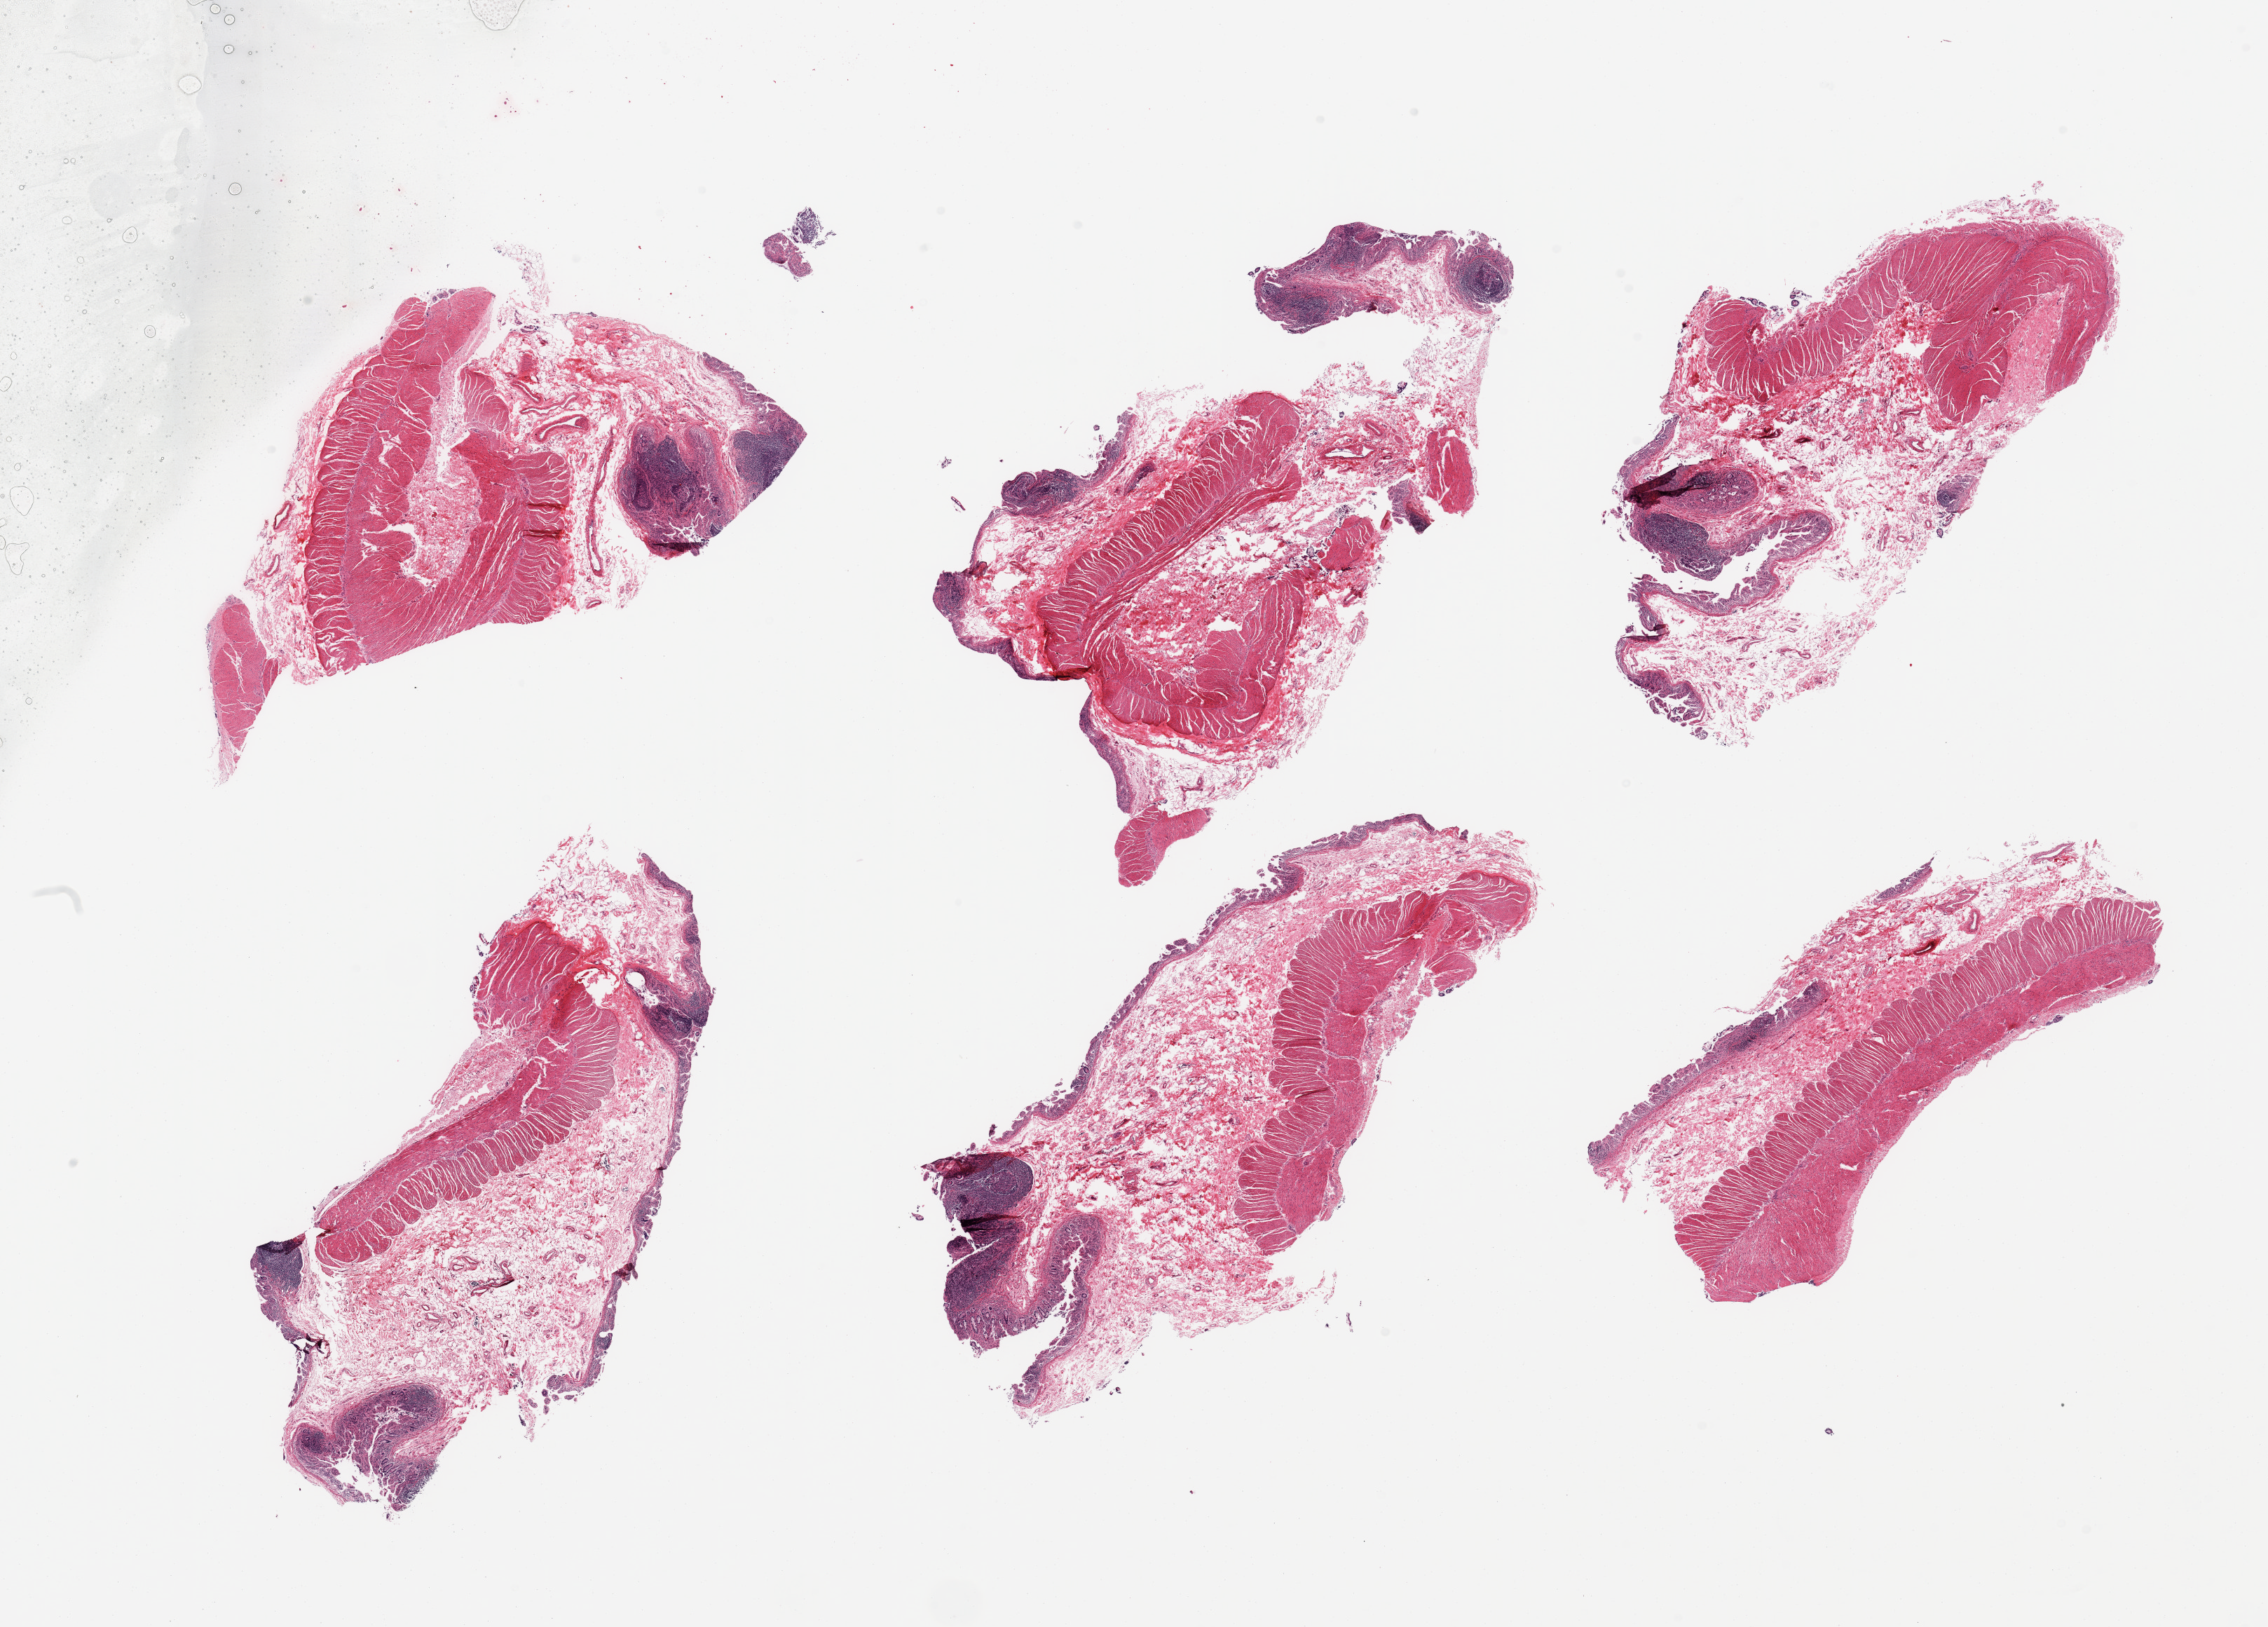
Hematoxylin and eosin (H&E) whole-slide image — low-resolution overview of the scanned area, about 25.6 x 18.4 mm (from a 20x scan). Donor sex: male.
Specimen: PAXgene-fixed, paraffin-embedded tissue; section of ileum (target tissue); donor tissue sample.